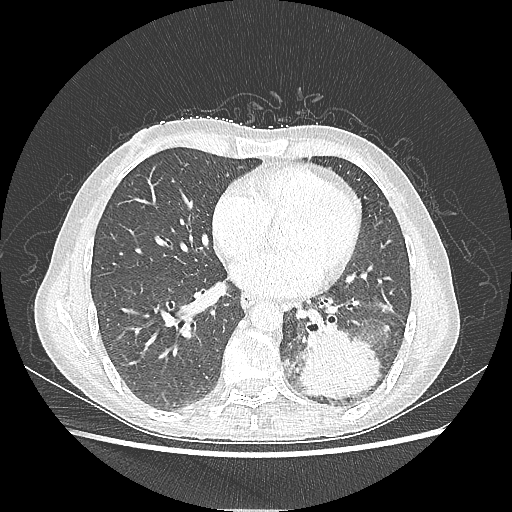
Chest CT, one axial slice; reconstruction kernel LUNG; lung window (W 1500 / L -600 HU); 1.25 mm slice thickness; 512 × 512 image matrix, field of view 360 × 360 mm. Female patient, age 53 years. From the clinical record (not read from this slice): clinical TNM (as recorded): T3 N0 M0.
Outlined on this slice (bounding box drawn by a radiologist):
- lung tumour (recorded histology: adenocarcinoma): bounding box [x1, y1, x2, y2] px = [297, 329, 382, 400]